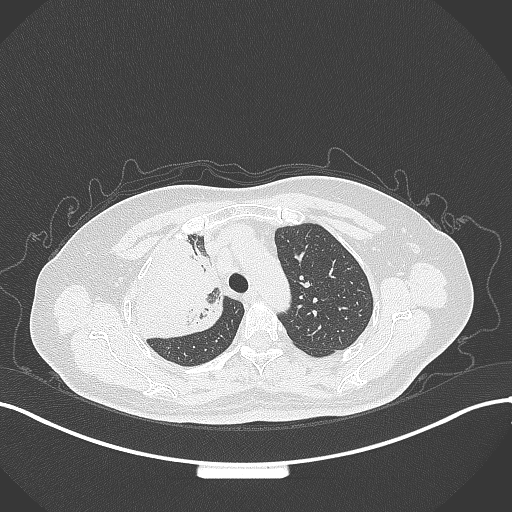
Chest CT, one axial slice; slice 240 of 309 in the series (ordered by position); lung window (W 1500 / L -600 HU); 1 mm slice thickness; 512 × 512 image matrix, field of view 400 × 400 mm. Patient: female, 60 years. Case-level facts recorded for this patient, not image findings: clinical TNM (as recorded): T3 N1 M1.
Annotated regions visible in this slice (bounding box drawn by a radiologist):
- lung tumour (recorded histology: adenocarcinoma): box from (x=118, y=230) to (x=227, y=343) px